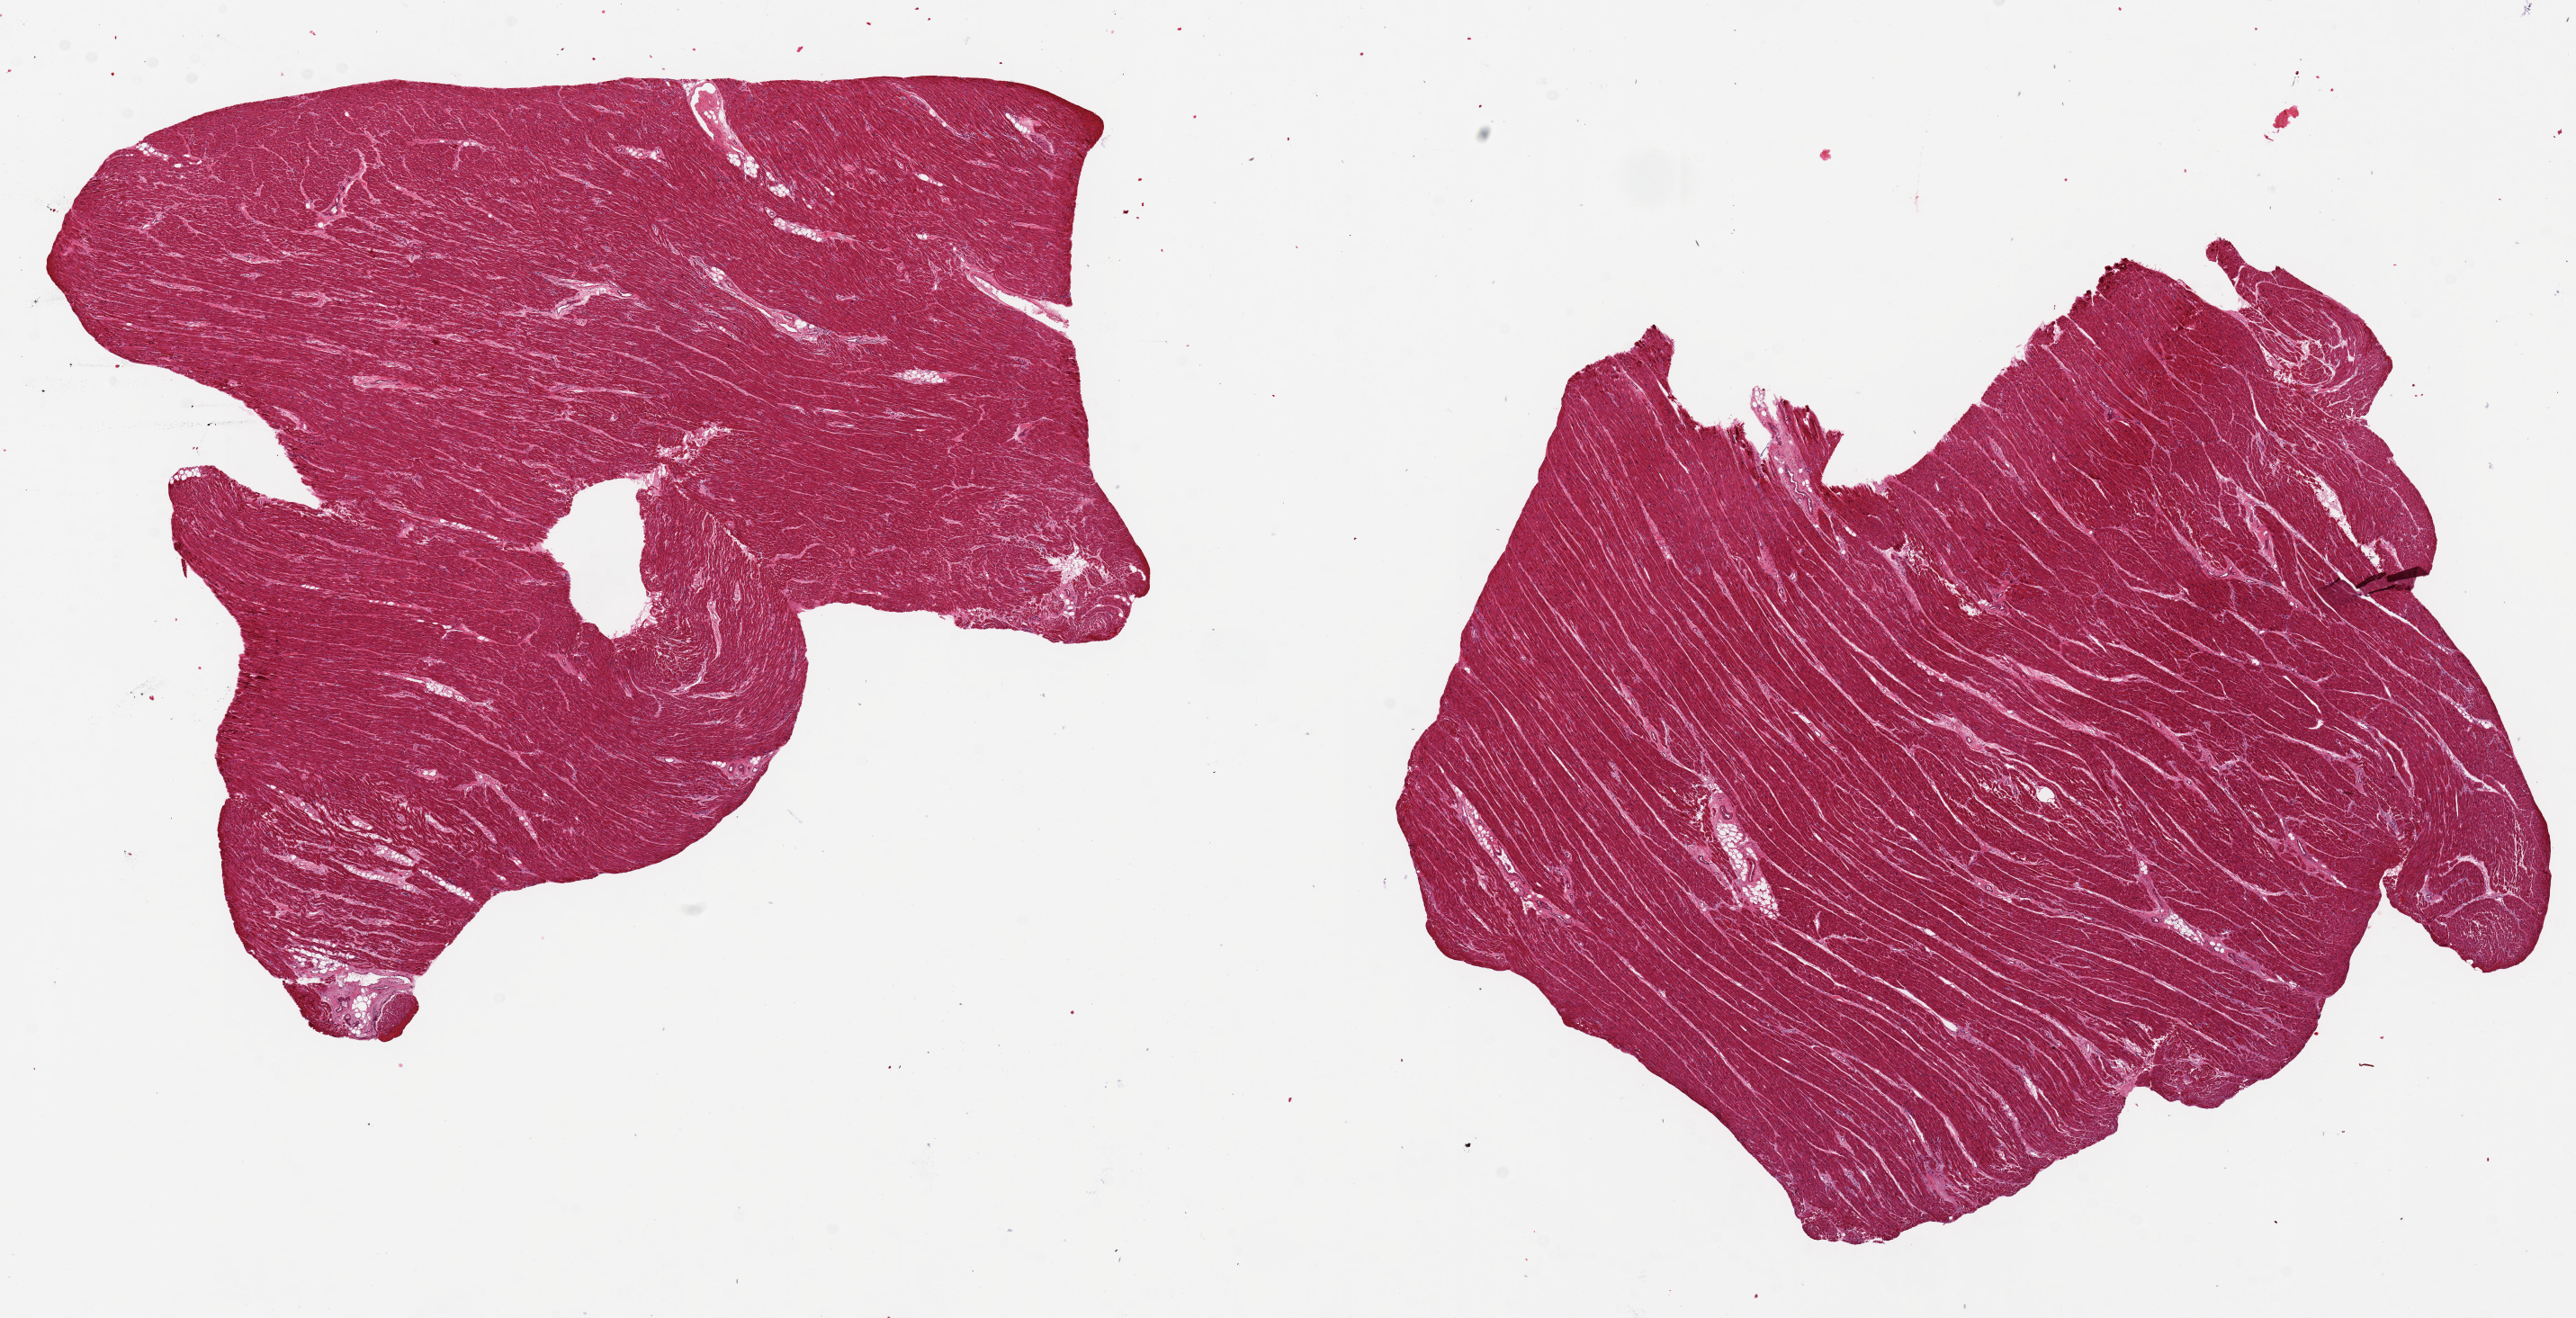
Hematoxylin and eosin (H&E) whole-slide image, brightfield, shown as a low-resolution overview of the whole scanned area (about 22.6 x 11.6 mm). PAXgene-fixed, paraffin-embedded tissue. Sampled site (target tissue): heart. Tissue donor sample. Donor sex: male.
Reviewer comment on this tissue sample: 2 pieces, 9x8 & 10x9mm; No extraneous tissue.